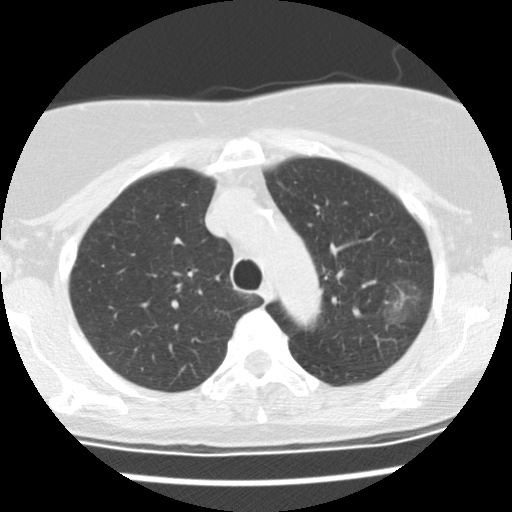
Axial slice from a low-dose chest CT screening exam. Baseline annual screen. Lung window (W 1500 / L -600 HU). 512 × 512 image matrix. Female participant, aged 66 years at enrolment.
• Expert-annotated lung lesion, bounding box [x1, y1, x2, y2] px = [380, 278, 426, 323].
• The exam's reader record, not a measurement of the box and not confirmed to be the same lesion: non-calcified nodule or mass ≥4 mm, left upper lobe, 25 × 17 mm, poorly defined margins, mixed attenuation.
• Official screen result: positive, change unspecified: nodule(s) >= 4 mm or enlarging nodule(s), mass(es), or other non-specific abnormalities suspicious for lung cancer.